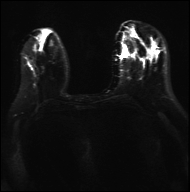
Breast MRI, one axial slice. Slice 10 of 36 in the series (ordered by position). Diffusion-weighted series; image 2 of 4 stored at this slice position (different b-values; order by instance number). 3 T. 4 mm slice thickness. 190 × 192 image matrix. Female patient.
Outlined on this slice (expert manual segmentation):
- tumour on diffusion-weighted imaging: bounding box <52,50,59,53> (left, top, right, bottom; pixels)